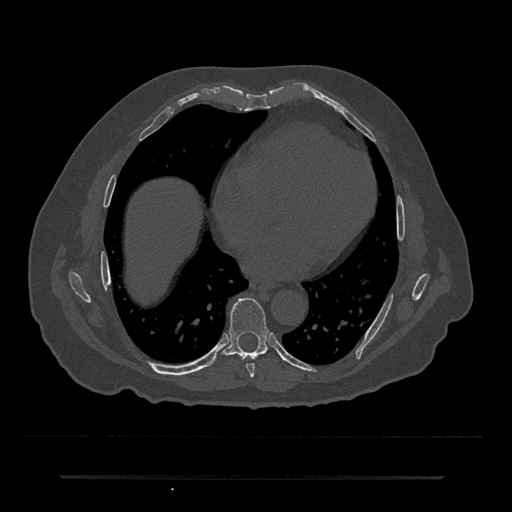
CT including the spine, one axial slice; position 349 of 797 along the scan axis; 120 kVp; bone window (W 1800 / L 400 HU); 0.5 mm slice thickness; 512 × 512 image matrix, field of view 437 × 437 mm. Patient: male, 69 years. Case-level facts recorded for this patient, not image findings: primary cancer: prostate.
Outlined on this slice (semi-automatic segmentation, software-assisted and operator-edited):
- T7 vertebra: bounding box <246,364,255,377> (left, top, right, bottom; pixels)
- T8 vertebra: <214,298,268,365>